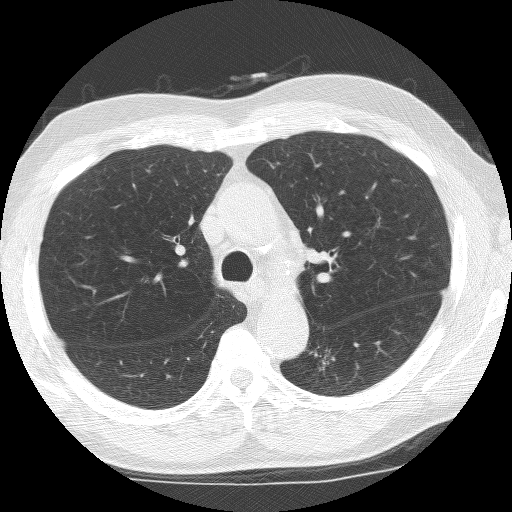
Low-dose screening chest CT, one axial slice; reconstruction kernel BONE; 120 kVp; lung window (W 1500 / L -600 HU); 2.5 mm slice thickness; 512 × 512 image matrix.
Outlined on this slice (manually delineated by an expert):
- lesion 1 (tumor, lower lobe of left lung): box from (x=314, y=347) to (x=335, y=370) px